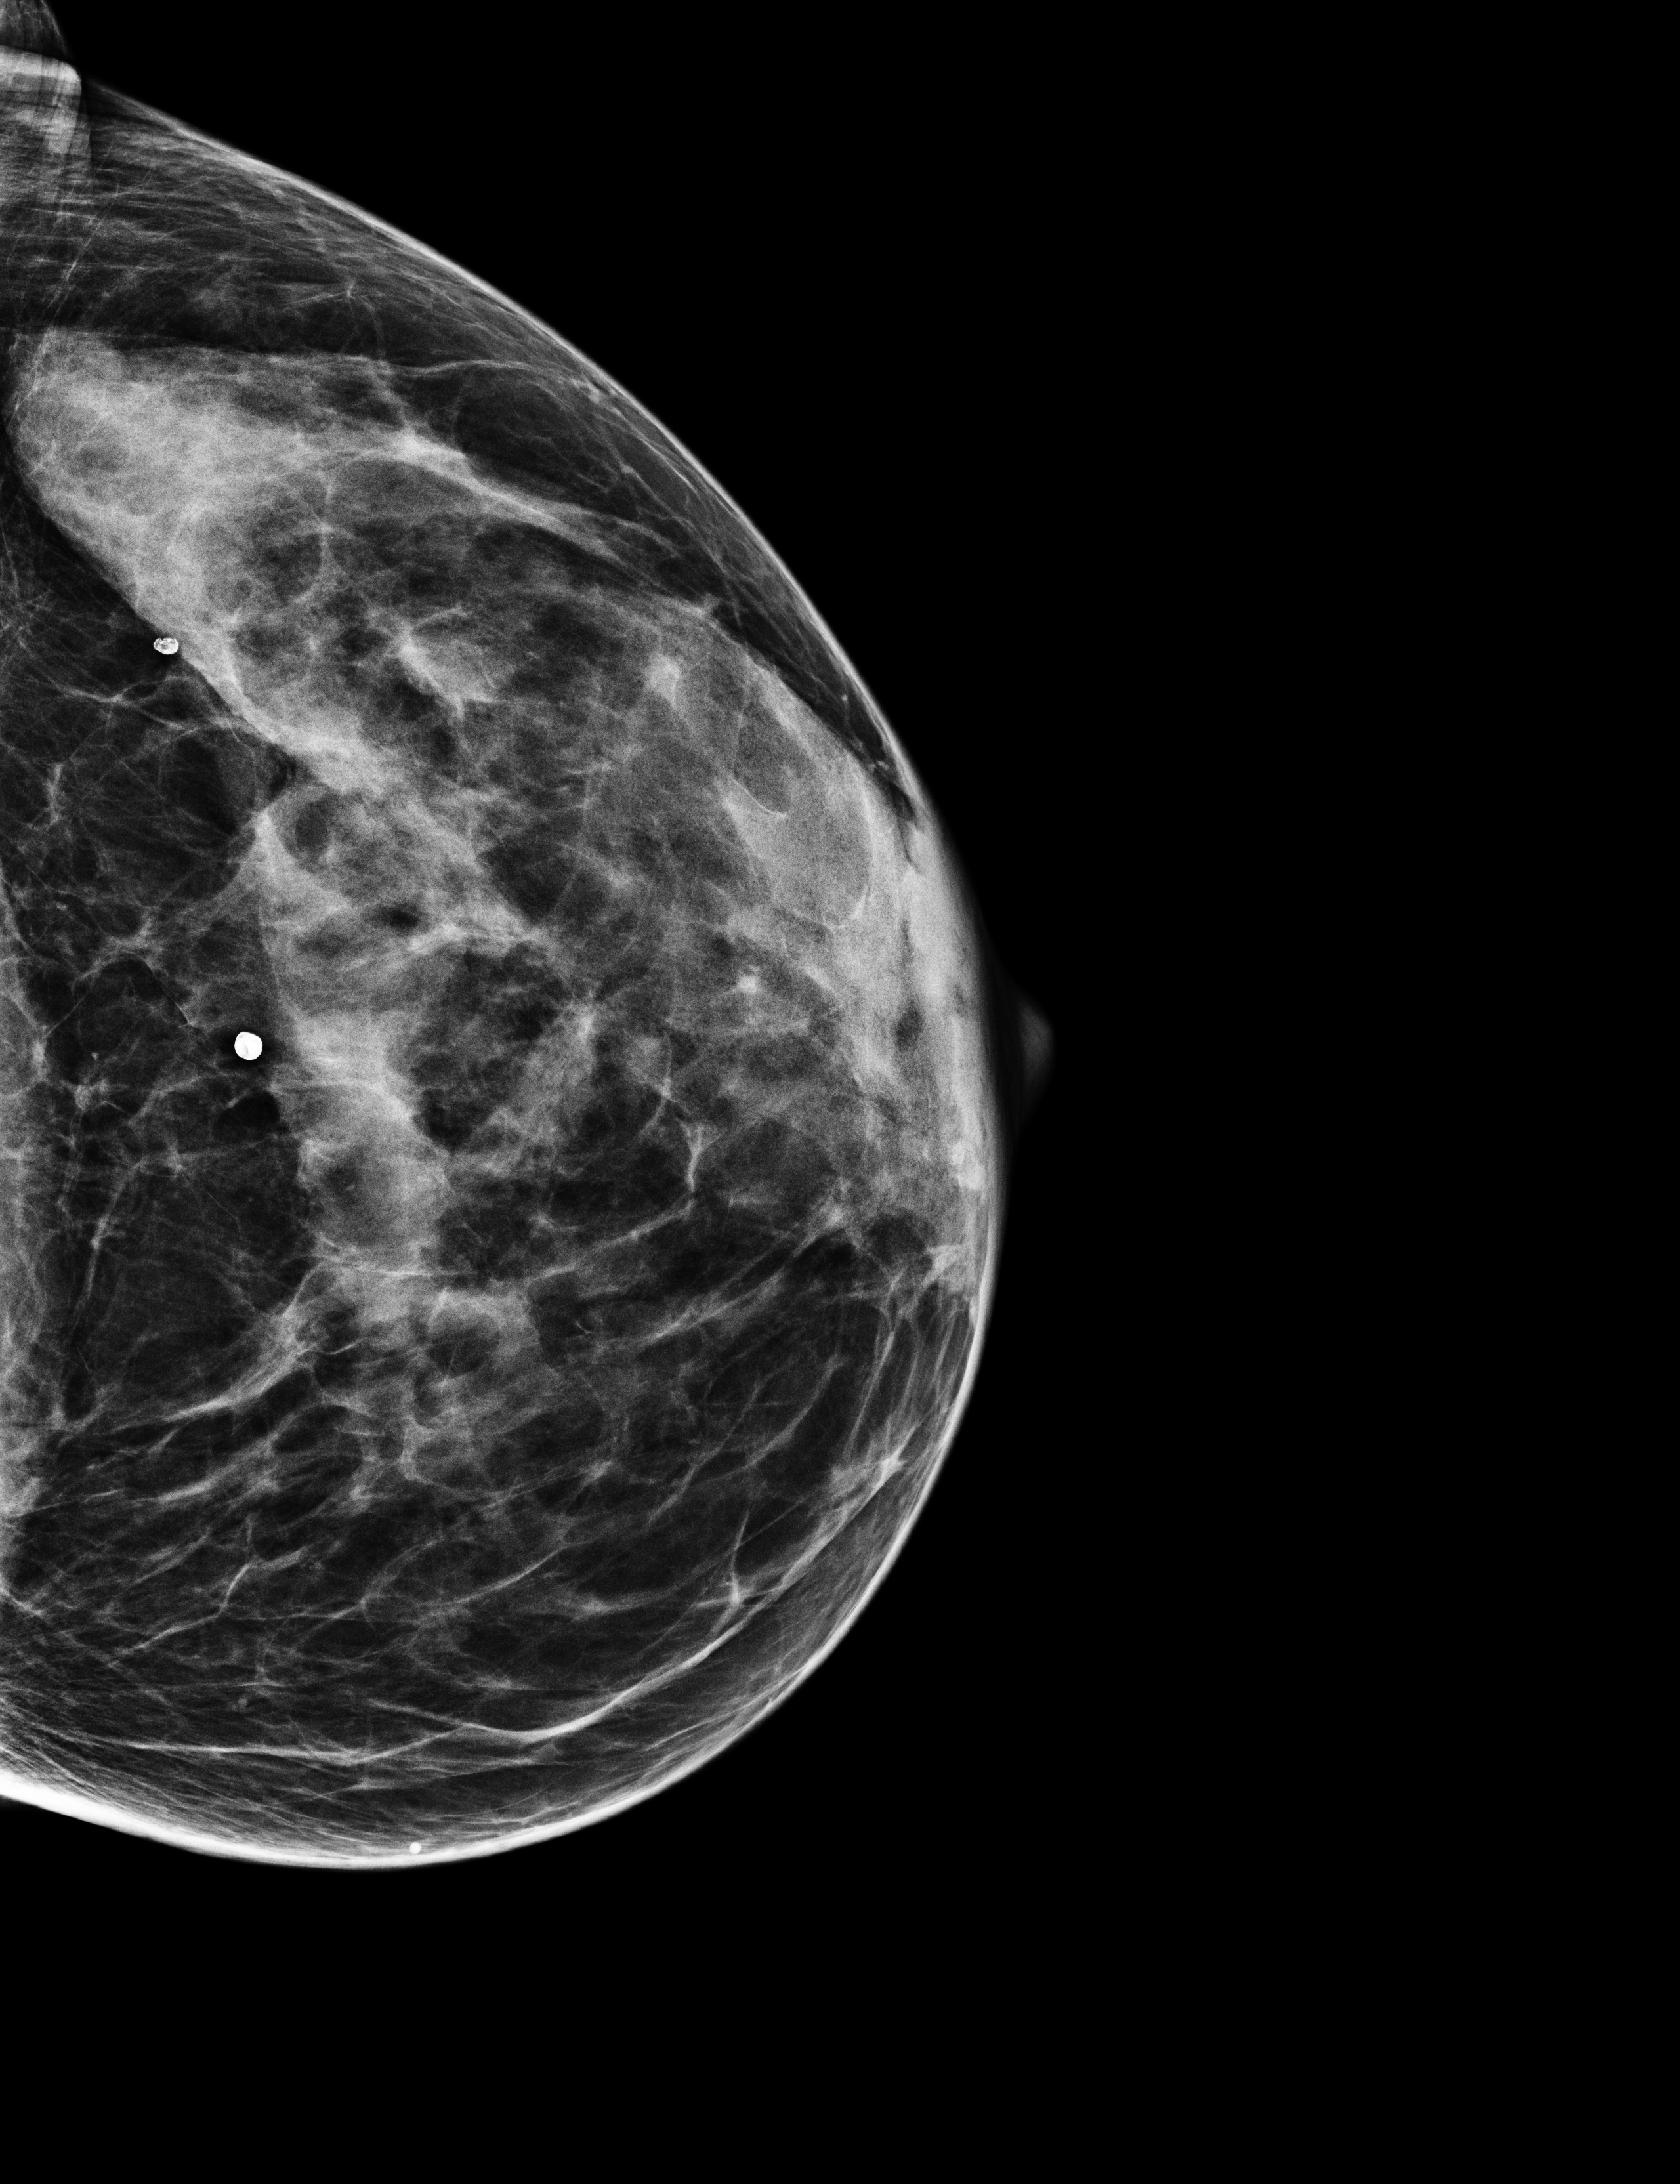
Screening examination, system: Selenia Dimensions. Female patient, age 55 years.
Image type: full-field digital mammogram. Breast: left. Projection: CC view.